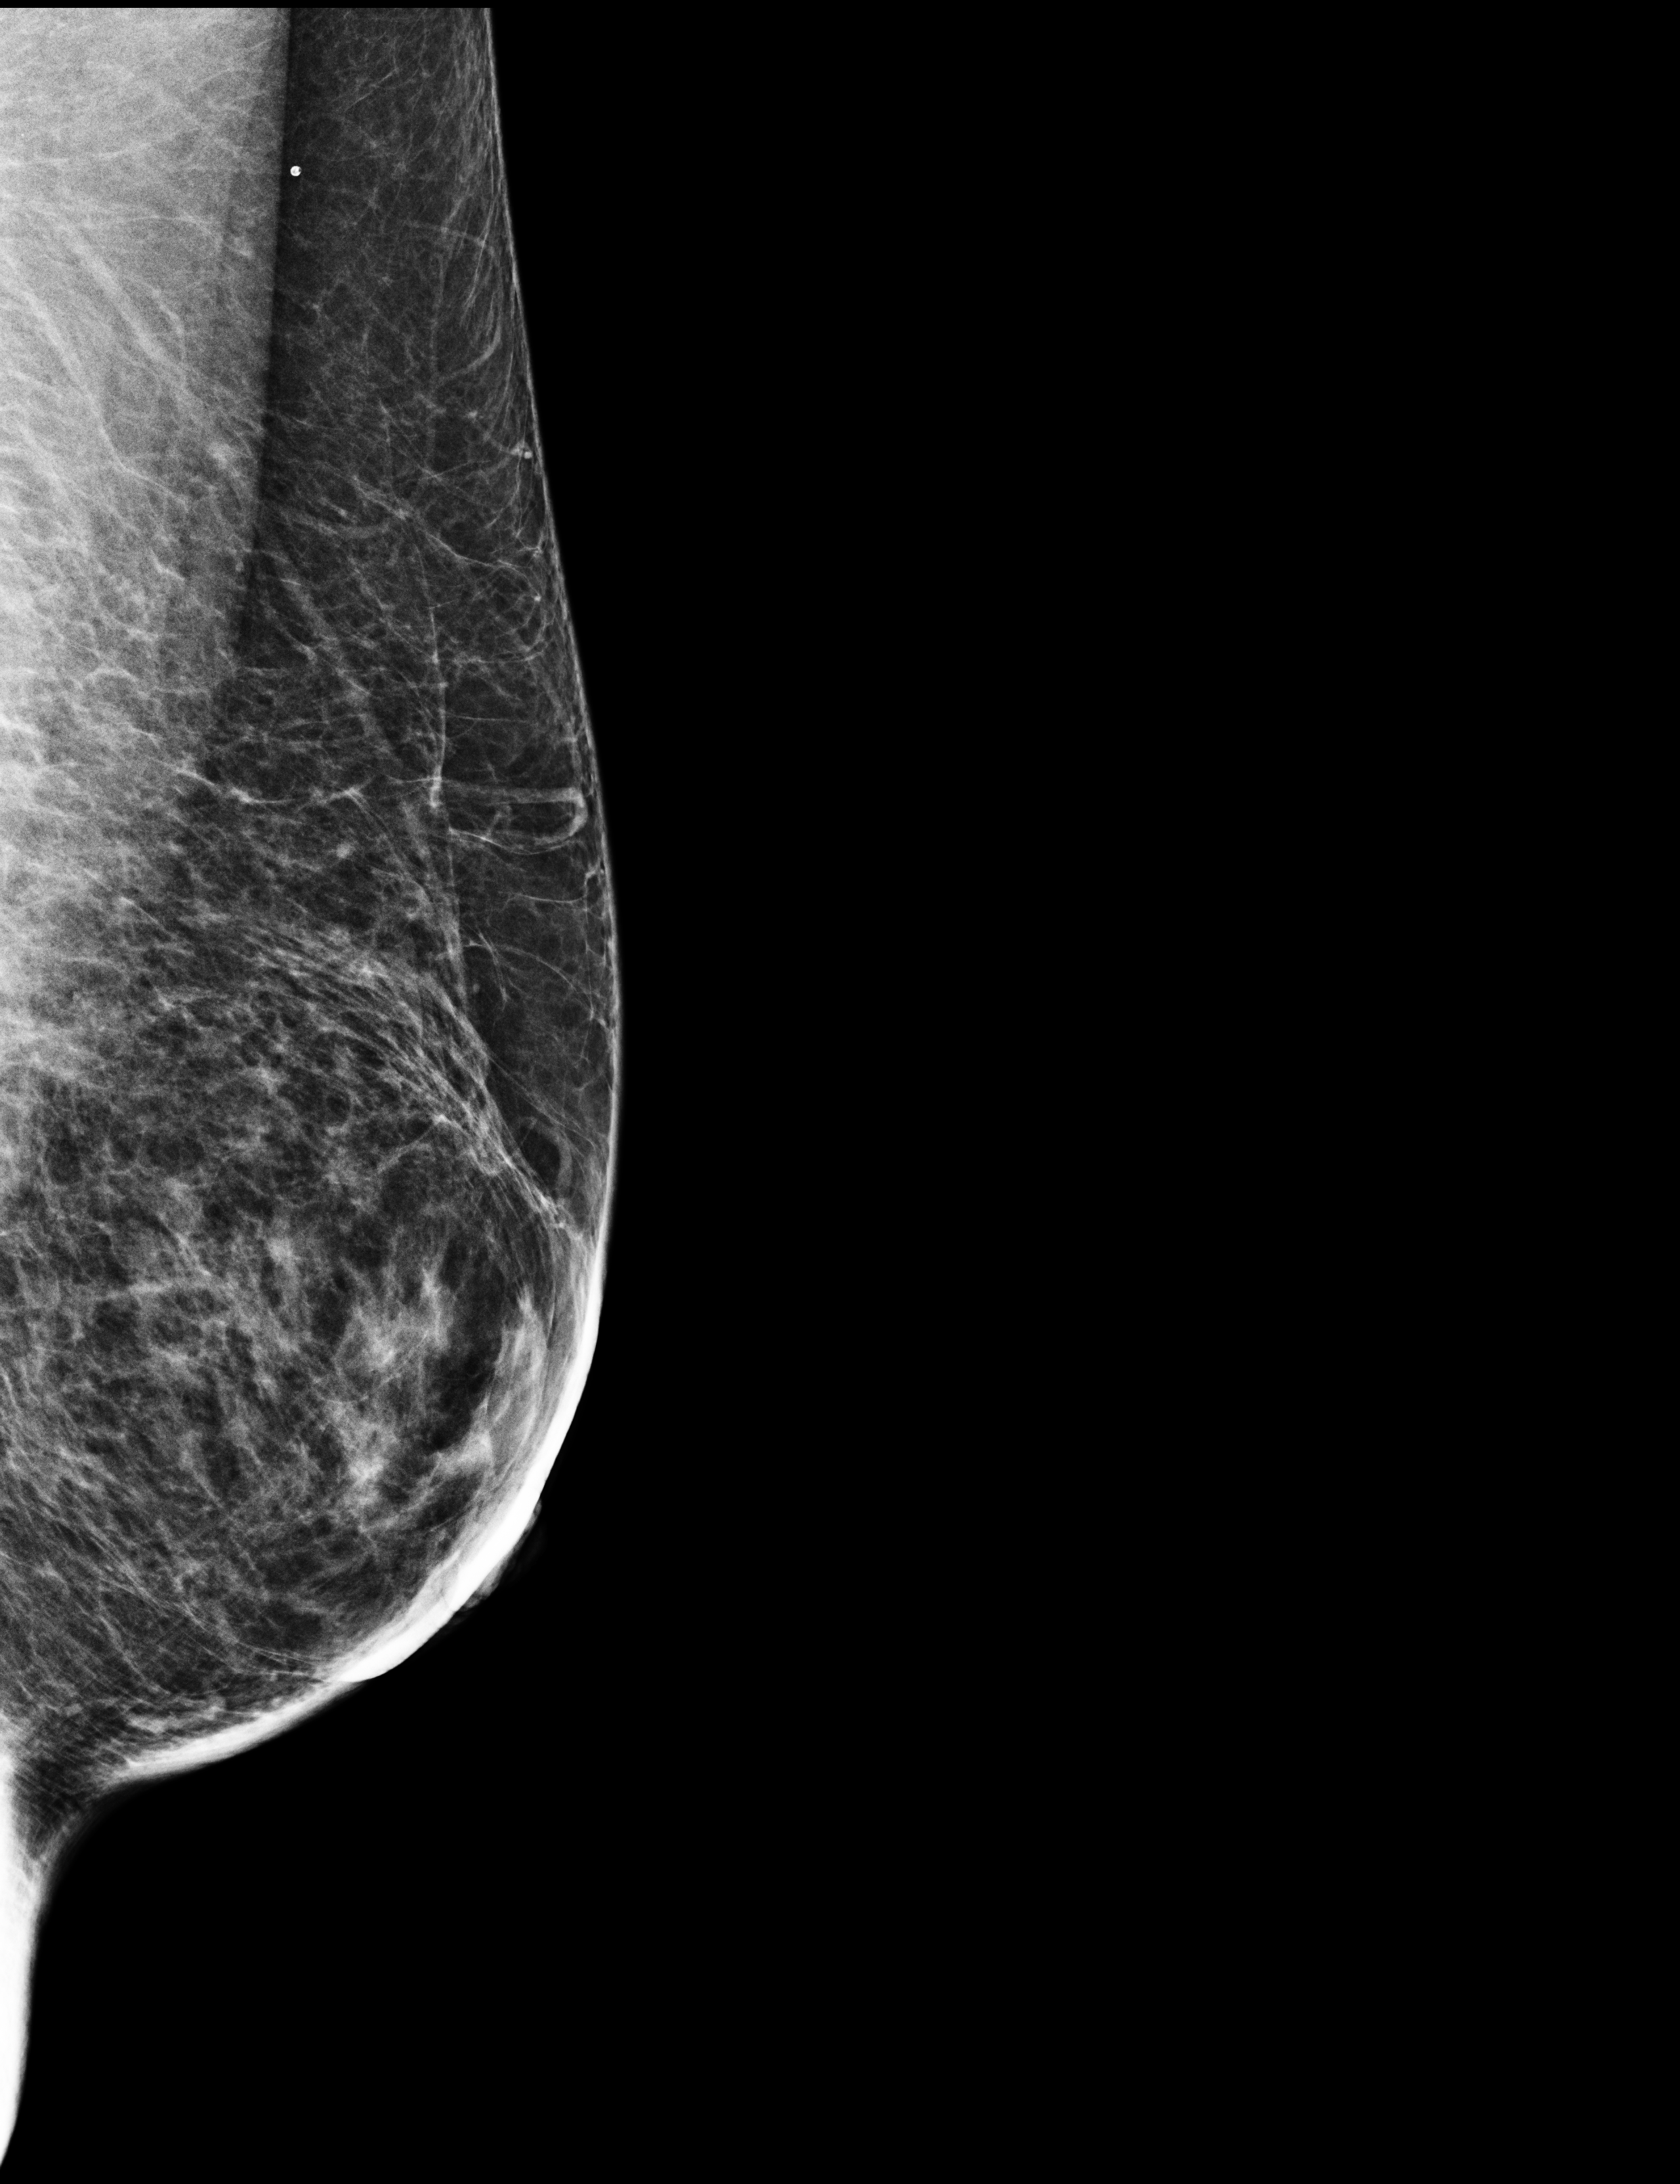
Annual screening mammography examination, compressed breast thickness 48 mm. Female patient, age 52 years.
Image type: full-field digital mammogram. Breast: left. Projection: medio-lateral oblique projection.